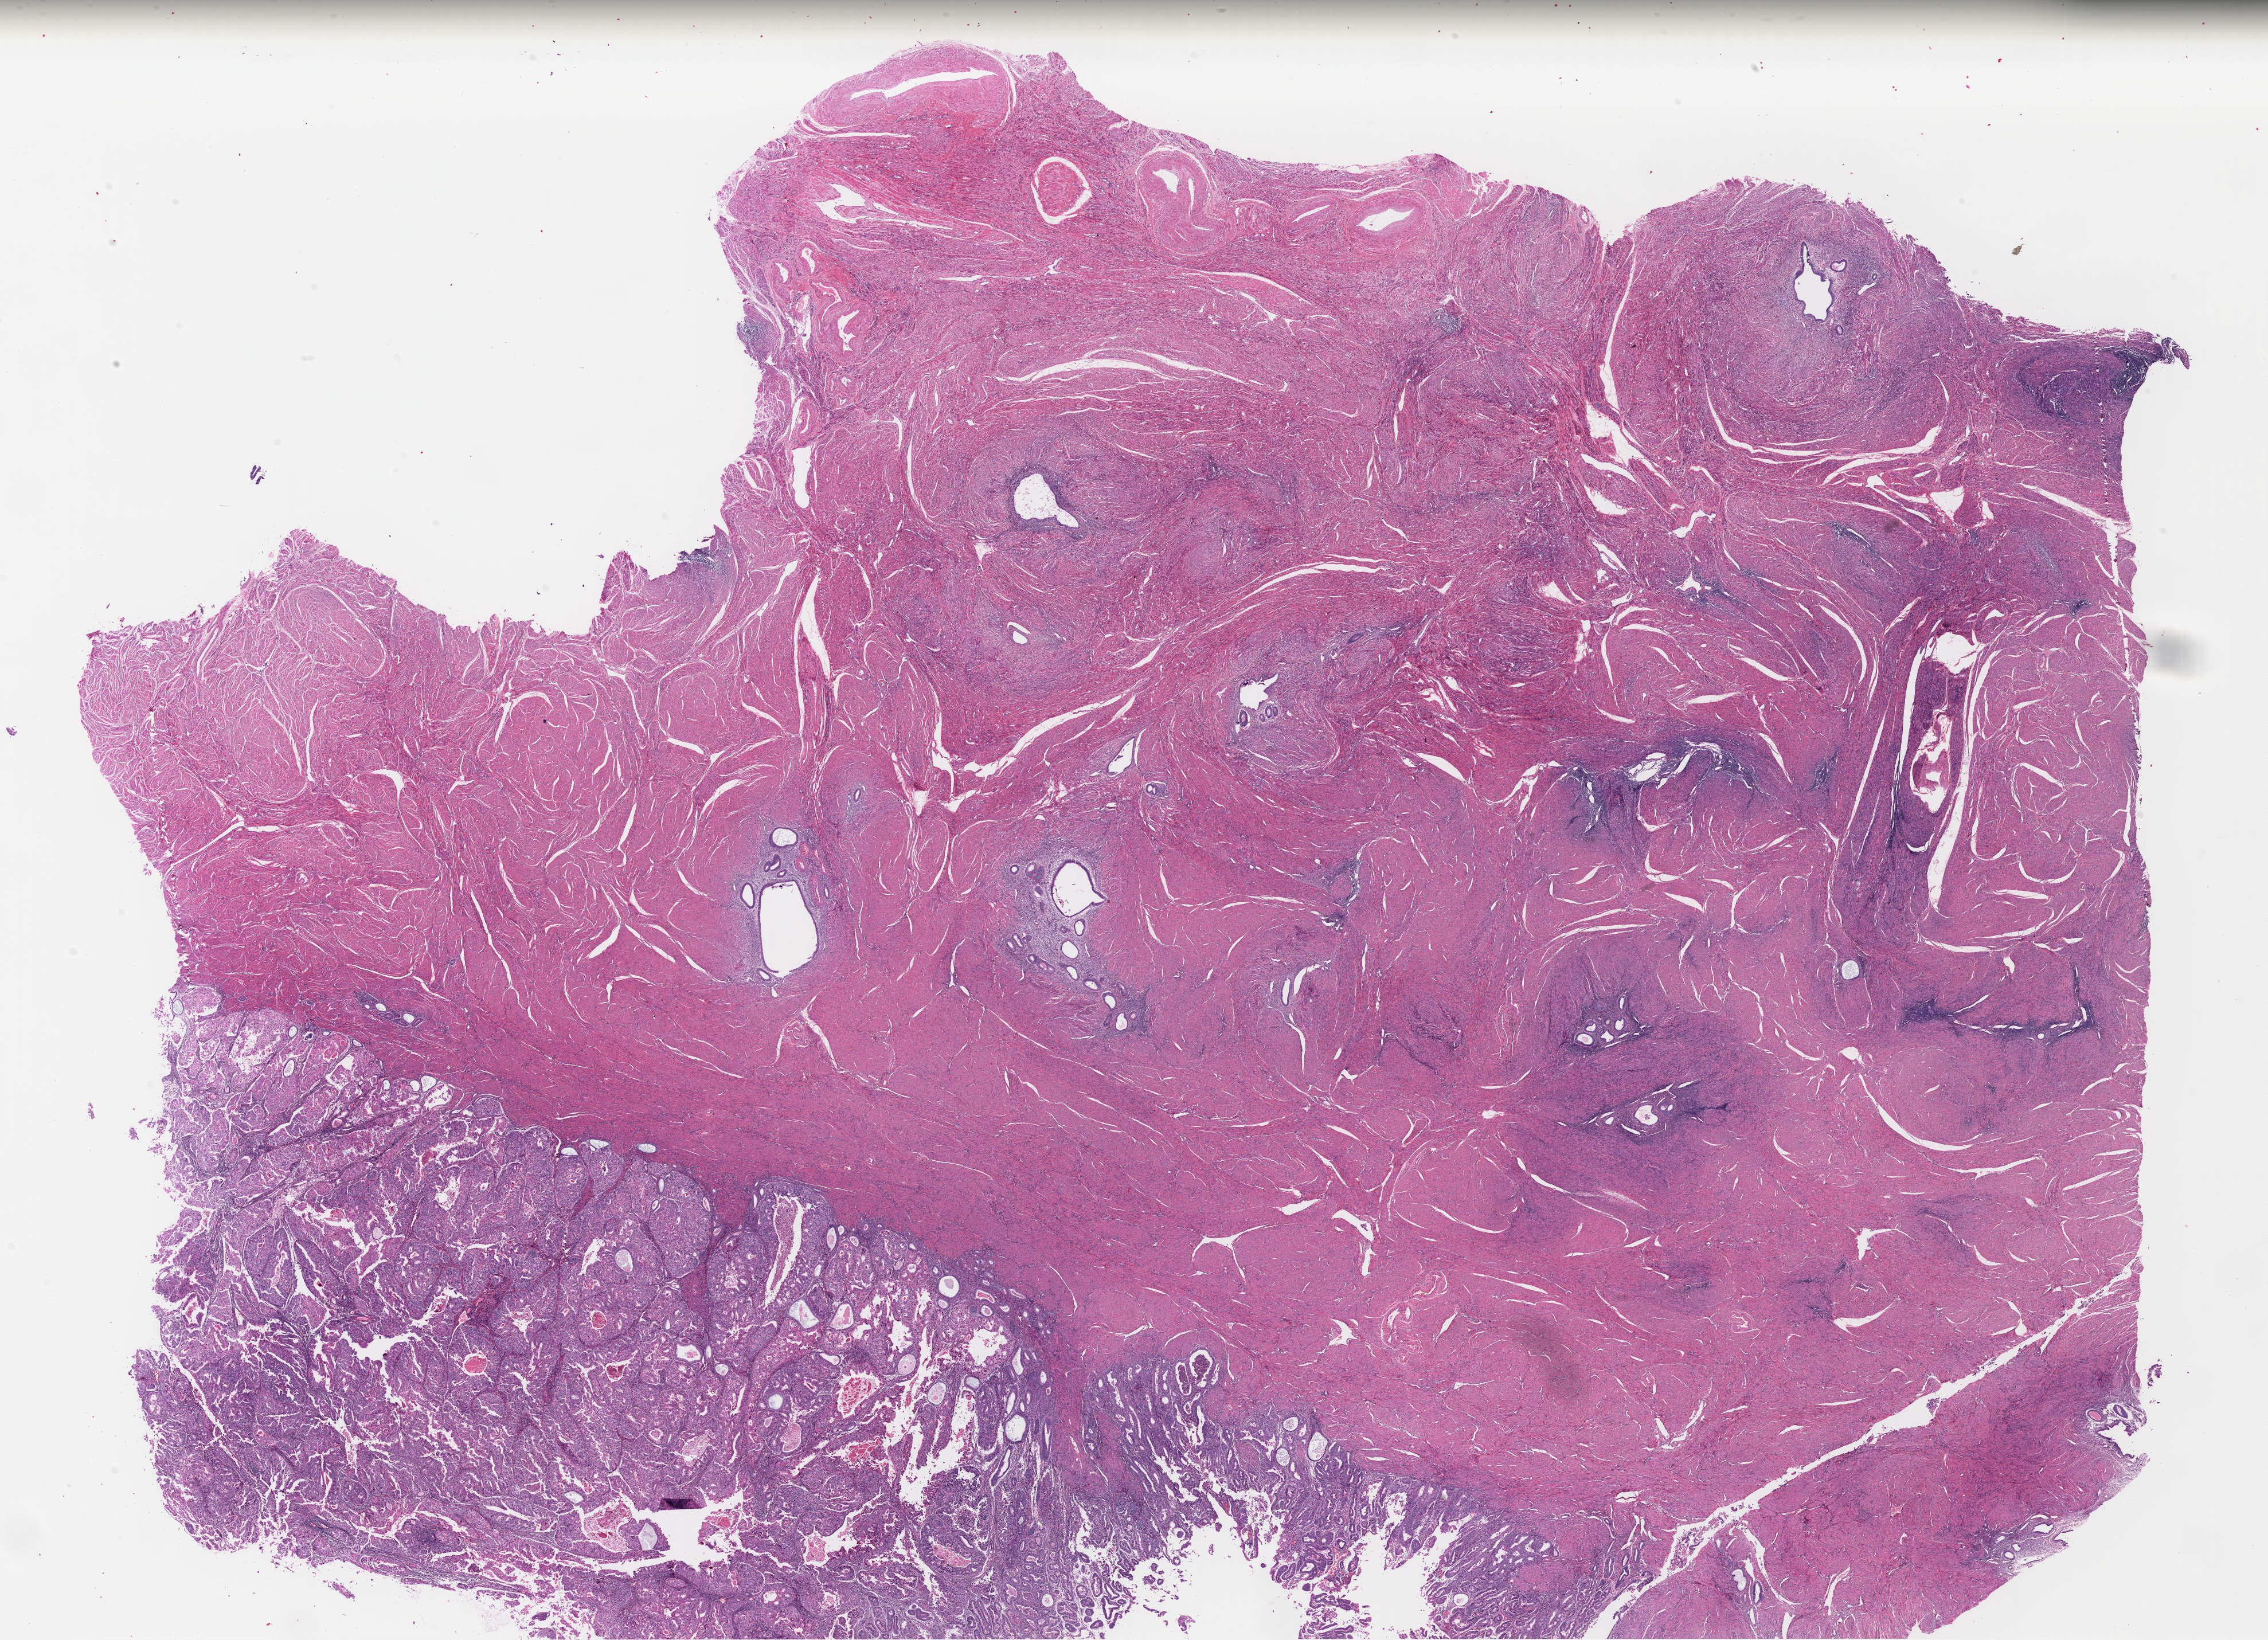
Digitized H&E-stained tissue section (whole slide) — shown as a low-resolution overview of the whole scanned area (about 31.1 x 22.5 mm, from a 40x scan), formalin-fixed paraffin-embedded (FFPE) diagnostic section, uterus, primary tumour sample. Female patient; age at initial diagnosis 56 years. Histologic grade: G3 (poorly differentiated).
Pathologic diagnosis: Endometrioid adenocarcinoma, NOS. FIGO stage: IB.